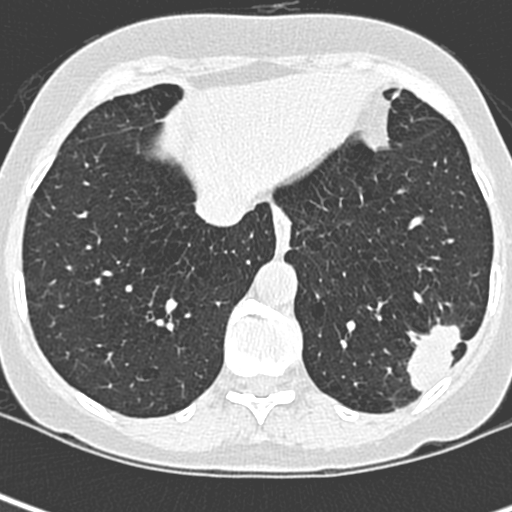
Low-dose screening chest CT, one axial slice. 120 kVp. Lung window (W 1500 / L -600 HU). 512 × 512 image matrix, field of view 271 × 271 mm.
Annotated regions visible in this slice (outlined manually by an expert reader):
- lesion 1 (tumor, lower lobe of left lung): bounding box <406,321,463,393> (left, top, right, bottom; pixels)